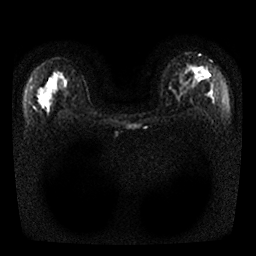
Breast MRI, one axial slice; slice 20 of 25 in the series (ordered by position); diffusion-weighted series; image 2 of 4 stored at this slice position (different b-values; order by instance number); 1.5 T; 4 mm slice thickness; 256 × 256 image matrix, field of view 320 × 320 mm. Female patient.
Structures marked on this image (outlined manually by an expert reader):
- tumour on diffusion-weighted imaging: bounding box [x1, y1, x2, y2] px = [189, 64, 211, 85]